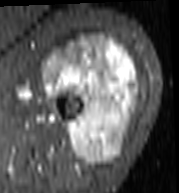
MRI of an extremity soft-tissue mass, one axial slice. Position 67 of 103 along the scan axis. STIR. MR volume resampled by the dataset authors to the PET/CT grid (not the native acquisition matrix). 3.27 mm slice thickness. 179 × 193 image matrix, field of view 175 × 188 mm. Female patient. From the clinical record (not read from this slice): histological type: undifferentiated – high grade; grade: high; site of the primary tumour: left thigh.
Outlined on this slice (expert contour drawn on MRI and transferred to this co-registered scan by the dataset authors):
- gross tumour volume including surrounding oedema: box from (x=43, y=35) to (x=140, y=166) px
- gross tumour volume (mass): (x=43, y=35)–(x=140, y=166)